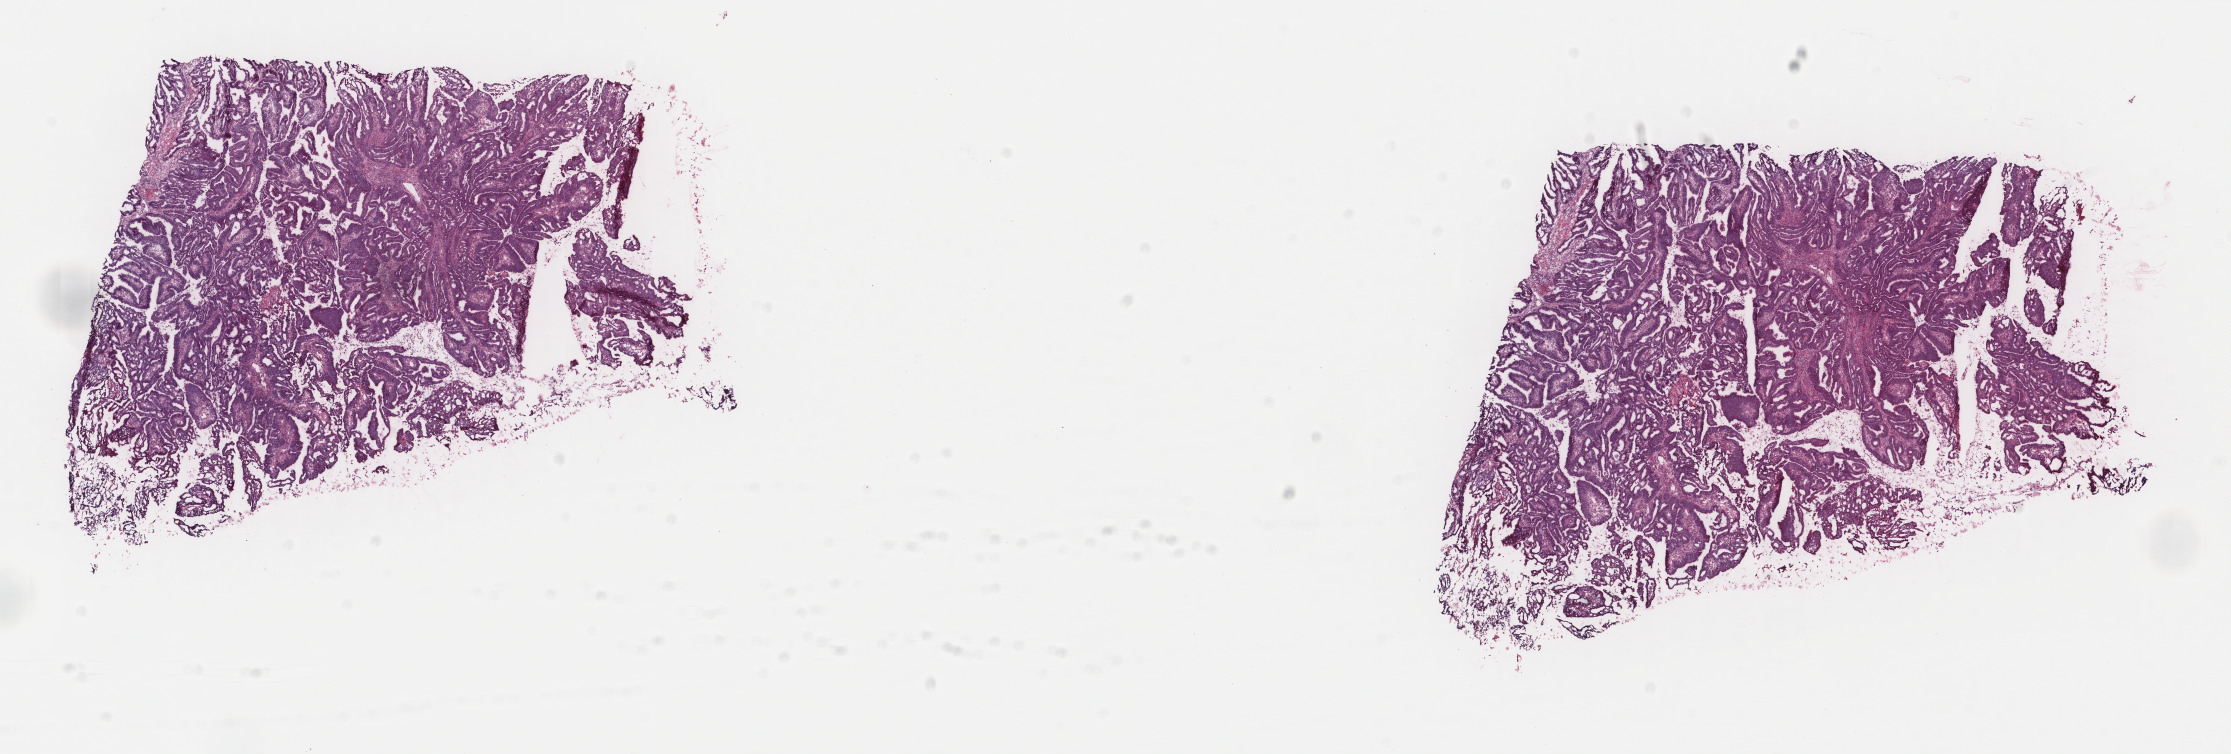
Hematoxylin and eosin (H&E) stained whole-slide image — whole scanned area (about 17.7 x 6.0 mm, acquisition: 40x scan) shown as a low-resolution overview. Frozen section from the top of the tissue portion. Primary tumour sample from the cervix. Female patient; age at initial diagnosis 32 years. Histologic grade: G2 (moderately differentiated). Pathologist review of this section (percent, as recorded): tumour cells 73%, tumour nuclei 70%, normal cells 0%, stromal cells 25%, necrosis 2%. Inflammatory infiltration, as recorded: lymphocyte infiltration 3%, monocyte infiltration 1%, neutrophil infiltration 20%.
FIGO stage: IB. Histologic diagnosis: Adenocarcinoma, endocervical type (cervix uteri).